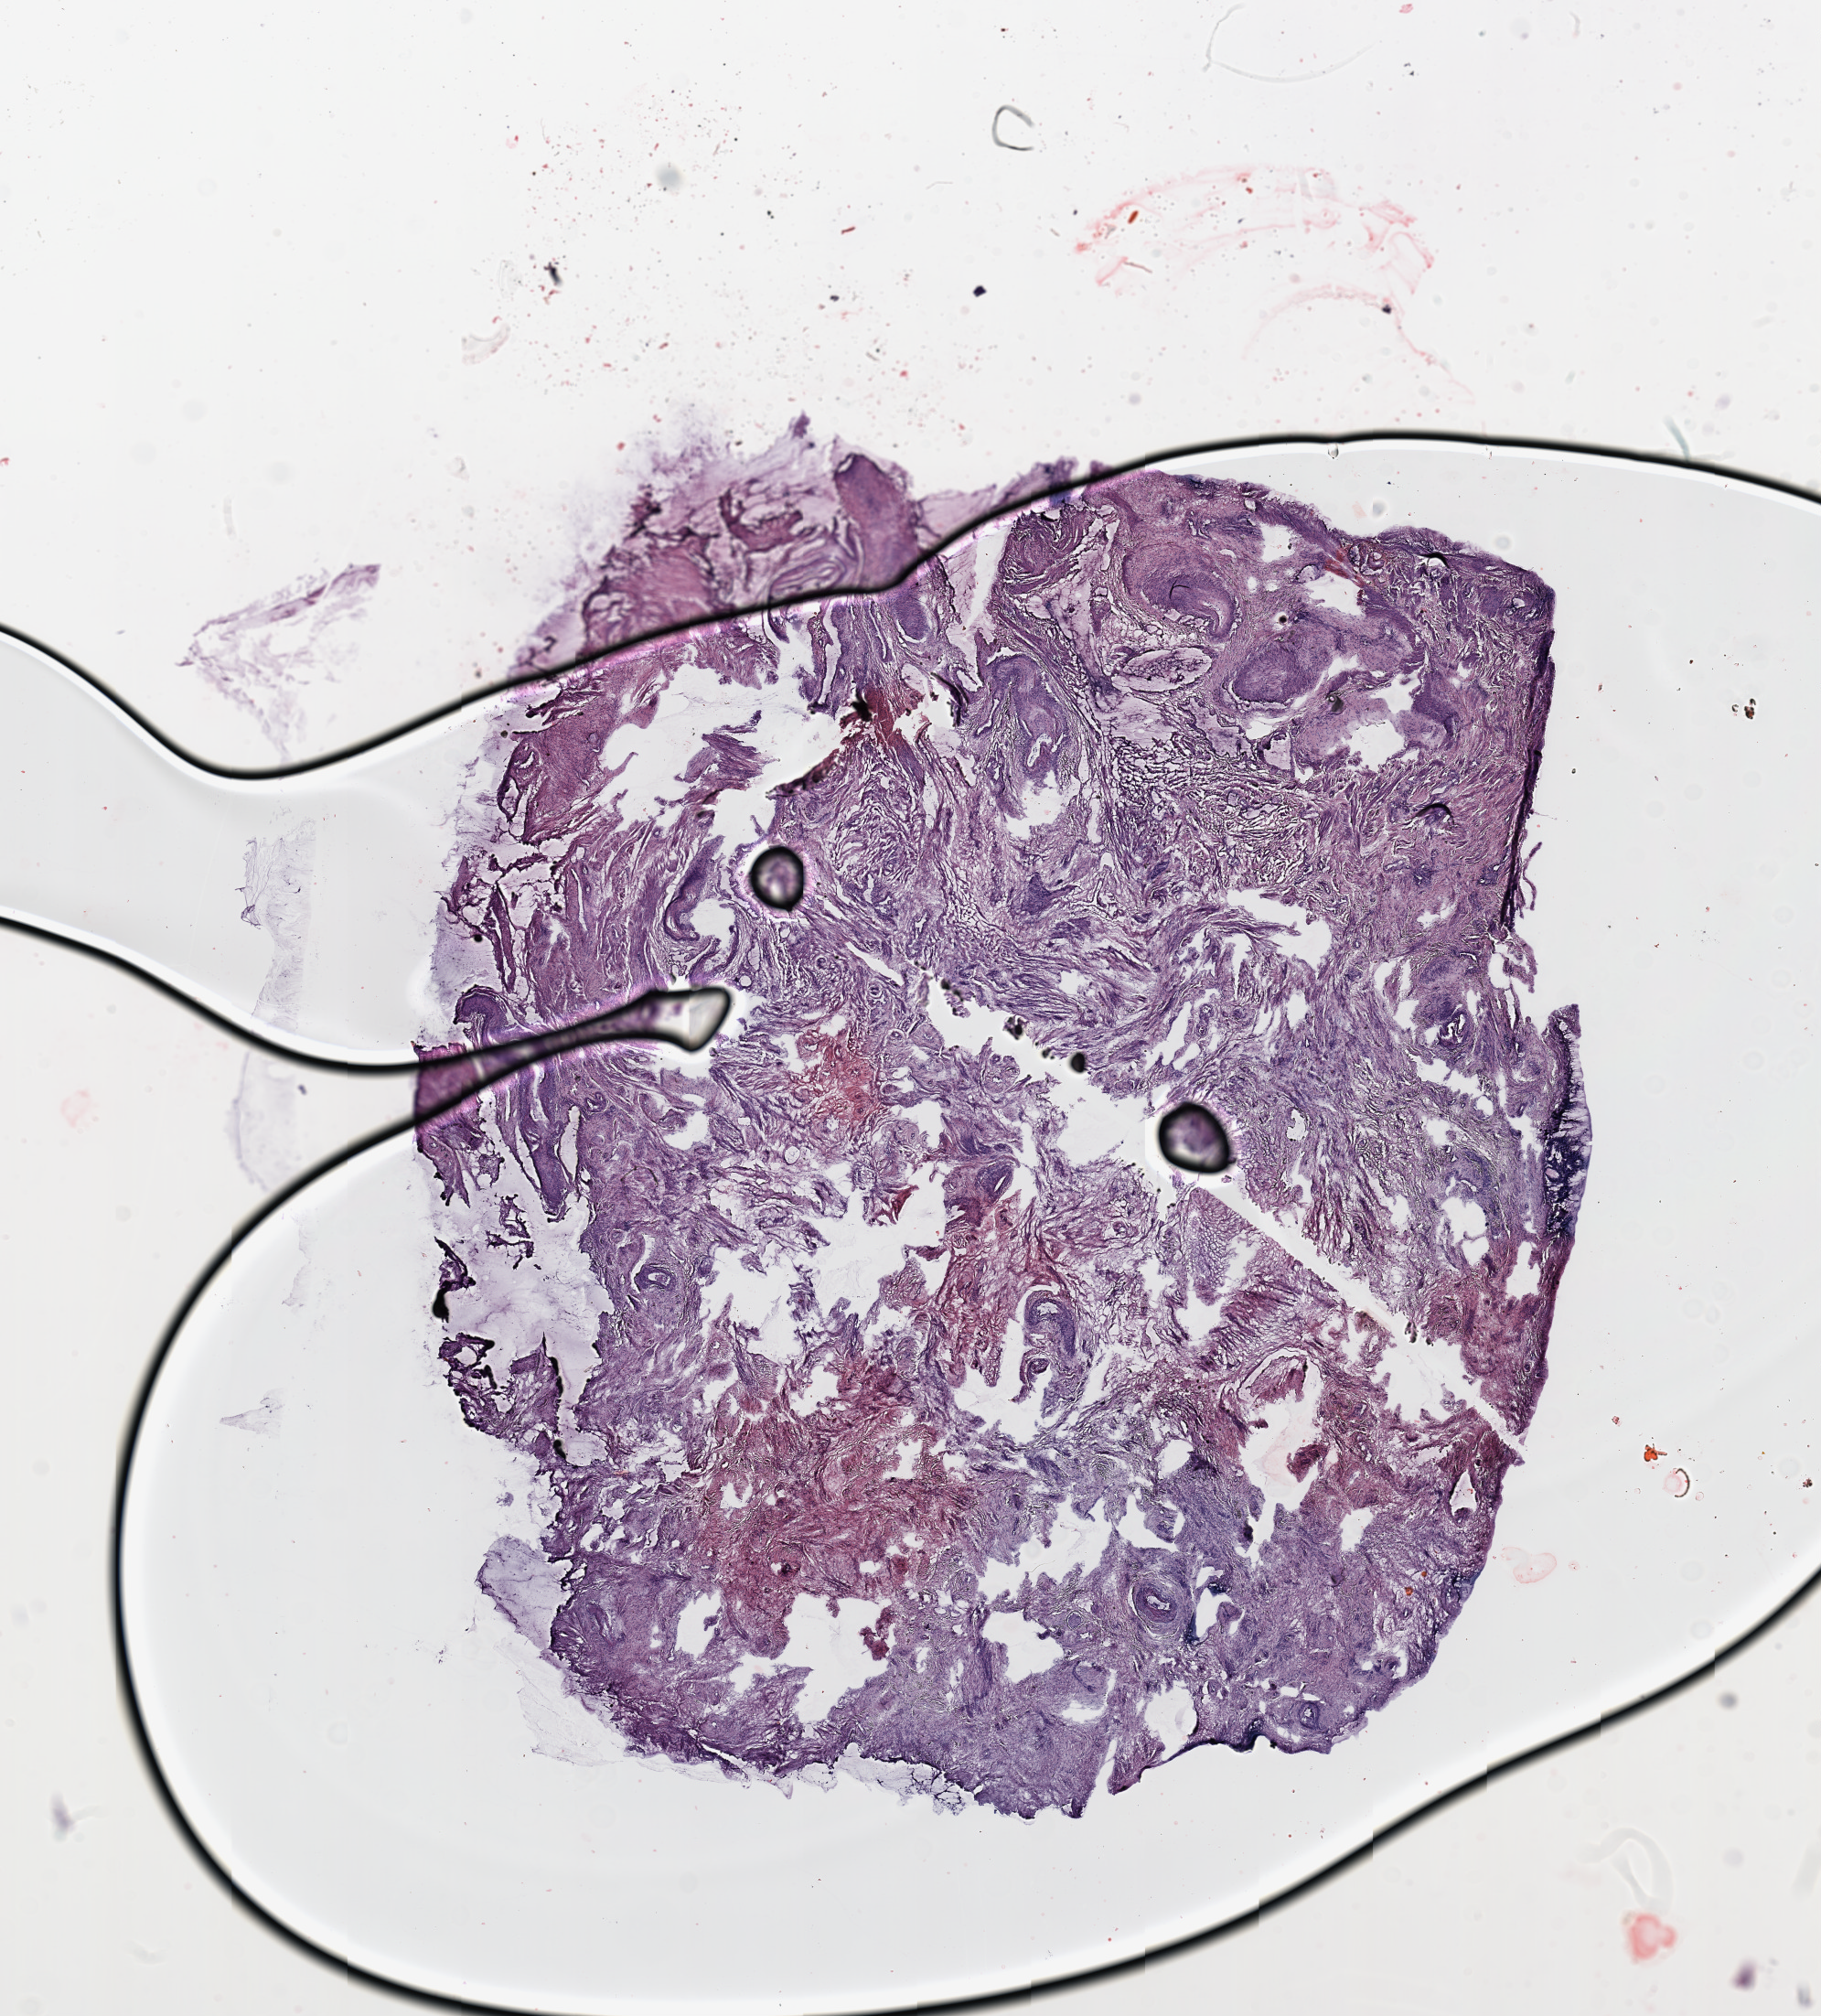
H&E whole-slide image — a low-resolution overview of the entire scanned area, about 15.8 x 17.4 mm (from a 20x scan); uterus, normal (non-tumour) tissue. Female, 64 y/o.
• this section: normal (non-tumour) tissue from the same patient
• patient diagnosis: Endometrioid adenocarcinoma, NOS